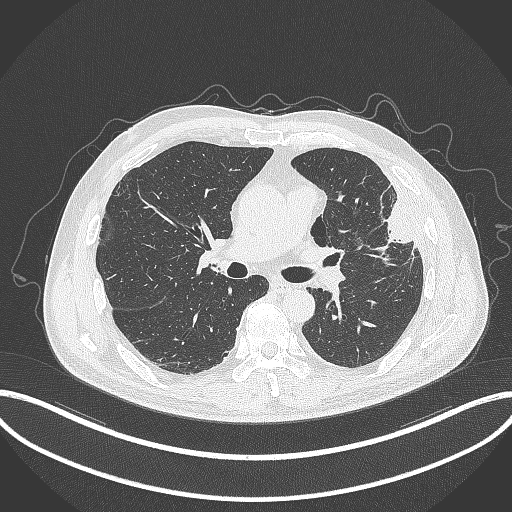
Chest CT, one axial slice; slice 193 of 382 in the series (ordered by position); reconstruction kernel B70f; 120 kVp; lung window (W 1500 / L -600 HU); 1 mm slice thickness; 512 × 512 image matrix. Patient: male, 64 years. Case-level facts recorded for this patient, not image findings: clinical TNM (as recorded): T4 N1 M0.
Structures marked on this image (rectangle marked by the reading radiologist):
- lung tumour (recorded histology: adenocarcinoma): bounding box <373,191,420,258> (left, top, right, bottom; pixels)